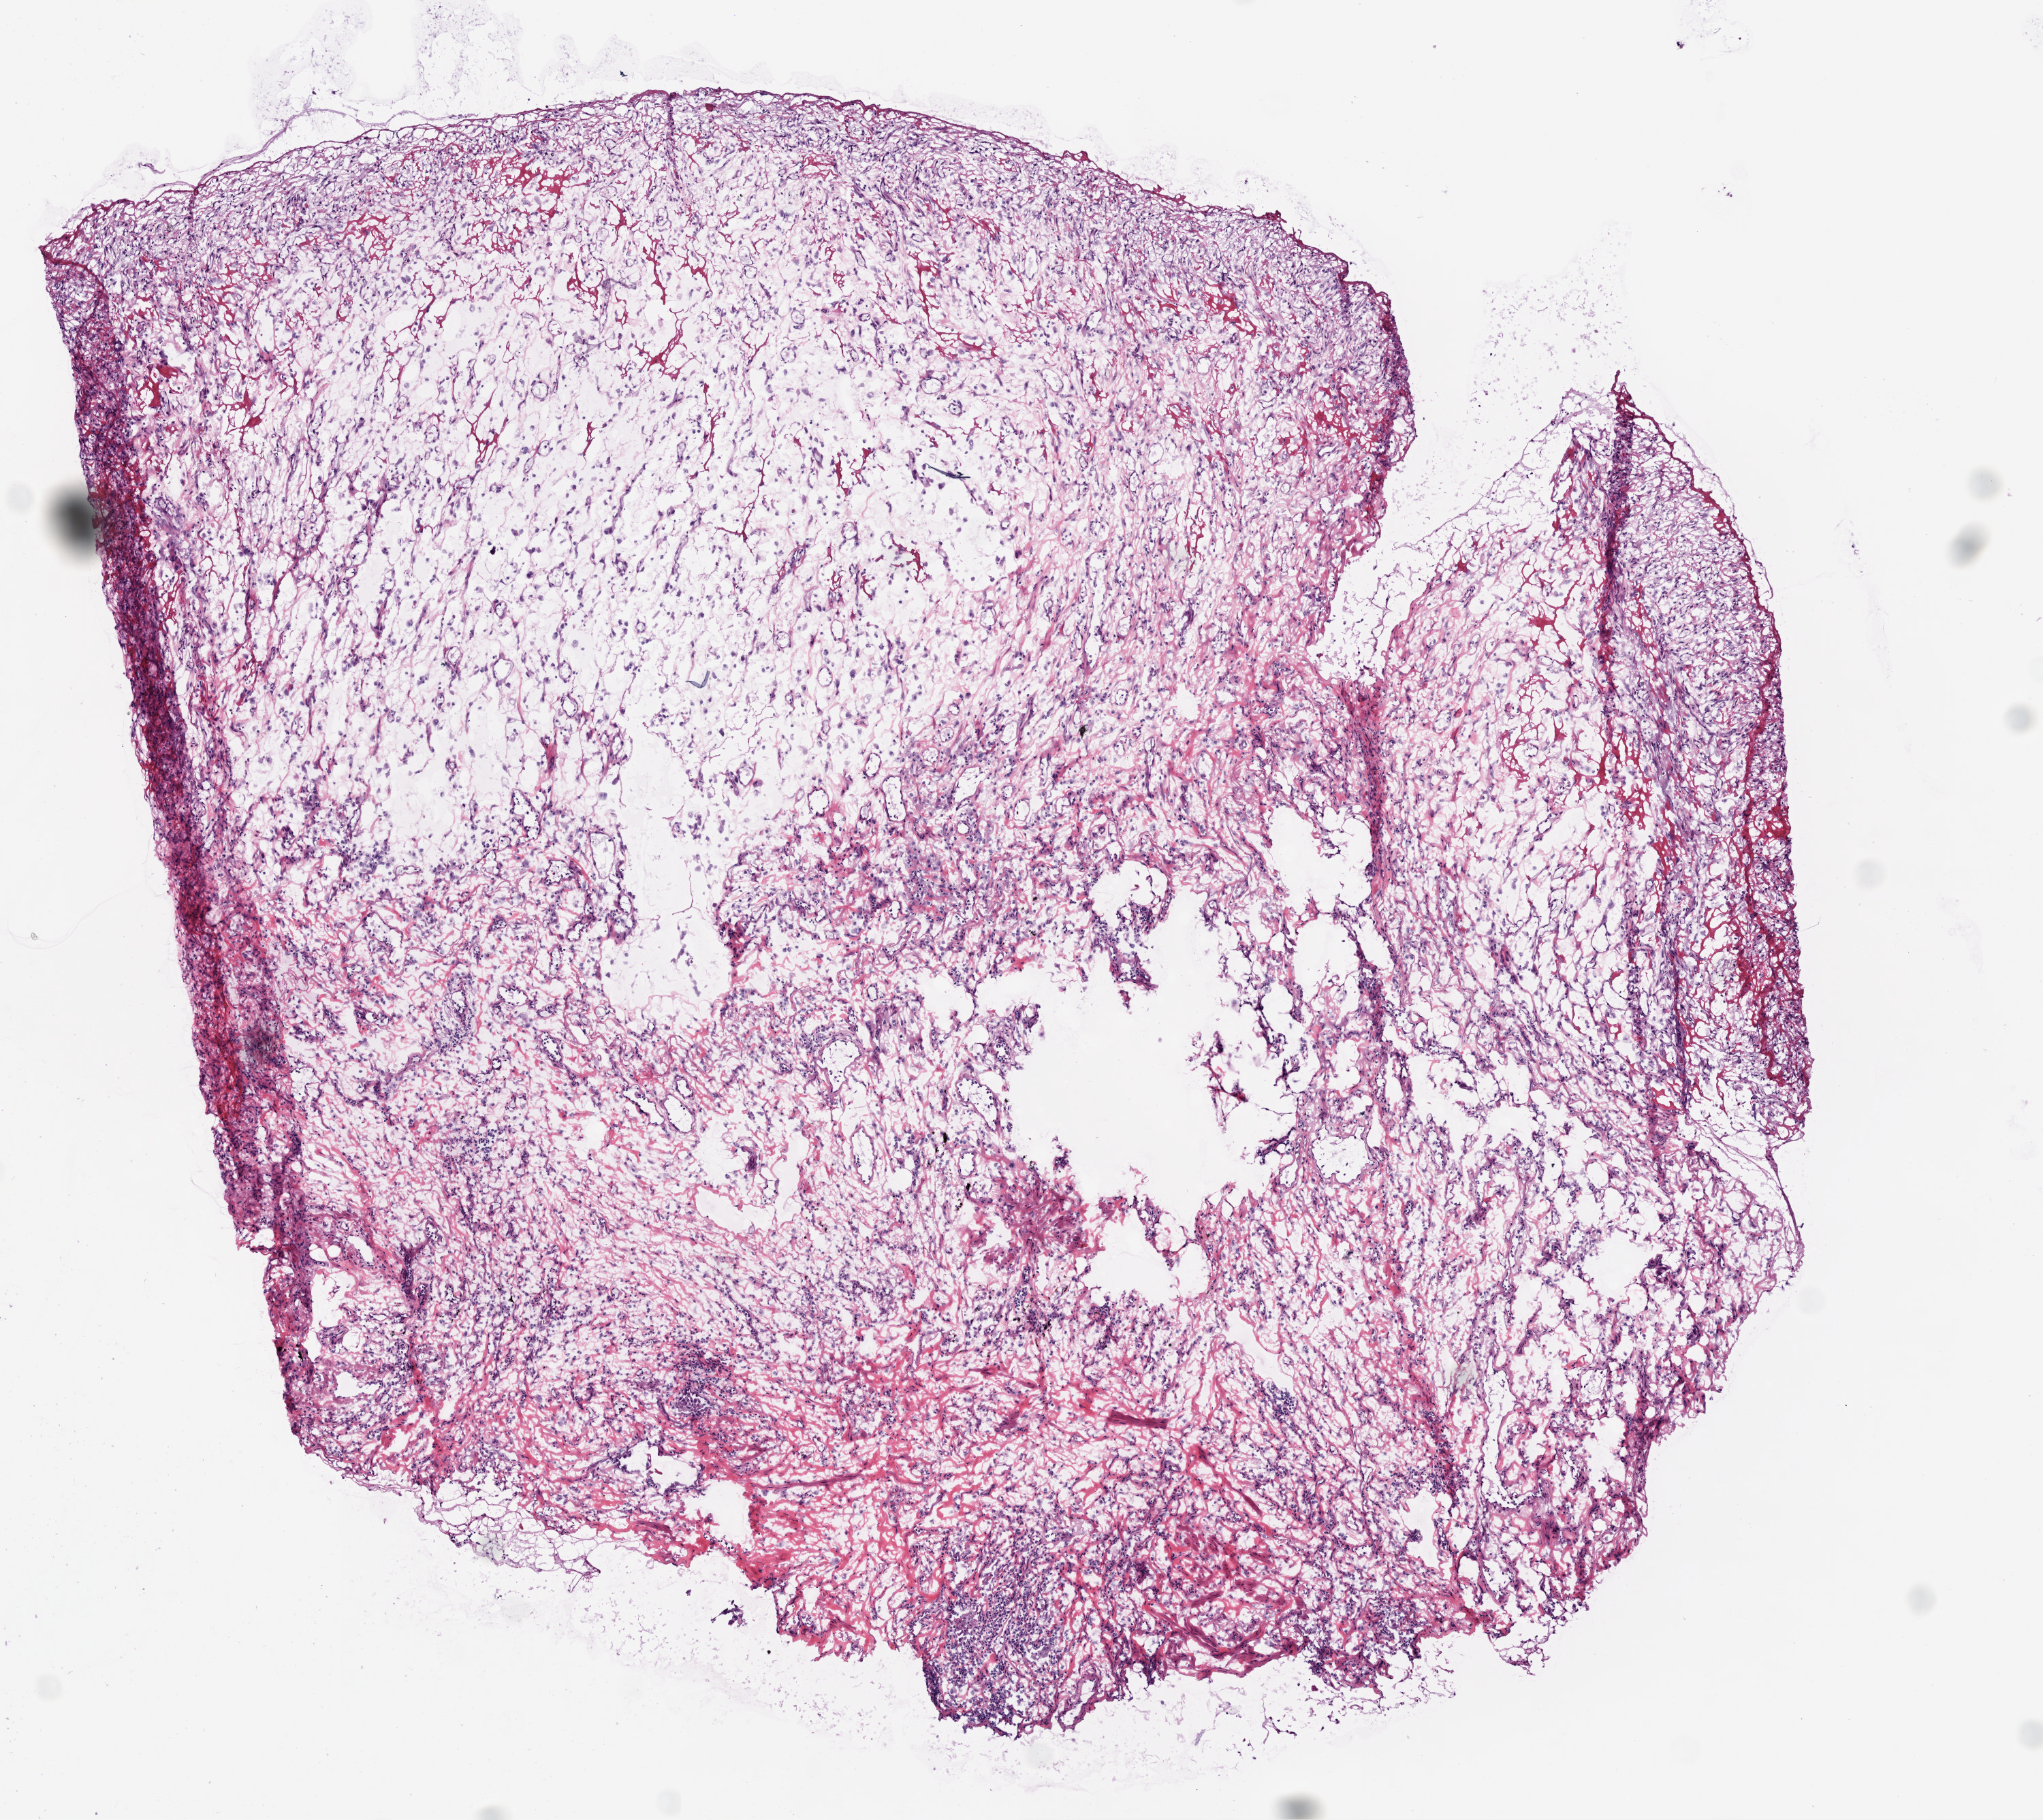
Digitized H&E-stained tissue section (whole slide), shown as a low-resolution overview of the whole scanned area (about 6.0 x 5.4 mm, acquisition: 20x scan), frozen section from the top of the tissue portion, lung, solid tissue normal (non-tumour tissue) sample. Patient: male, age at initial diagnosis 69 years.
This section: solid tissue normal (non-tumour) sample from the same patient. Patient diagnosis: Squamous cell carcinoma, NOS (lower lobe, lung).